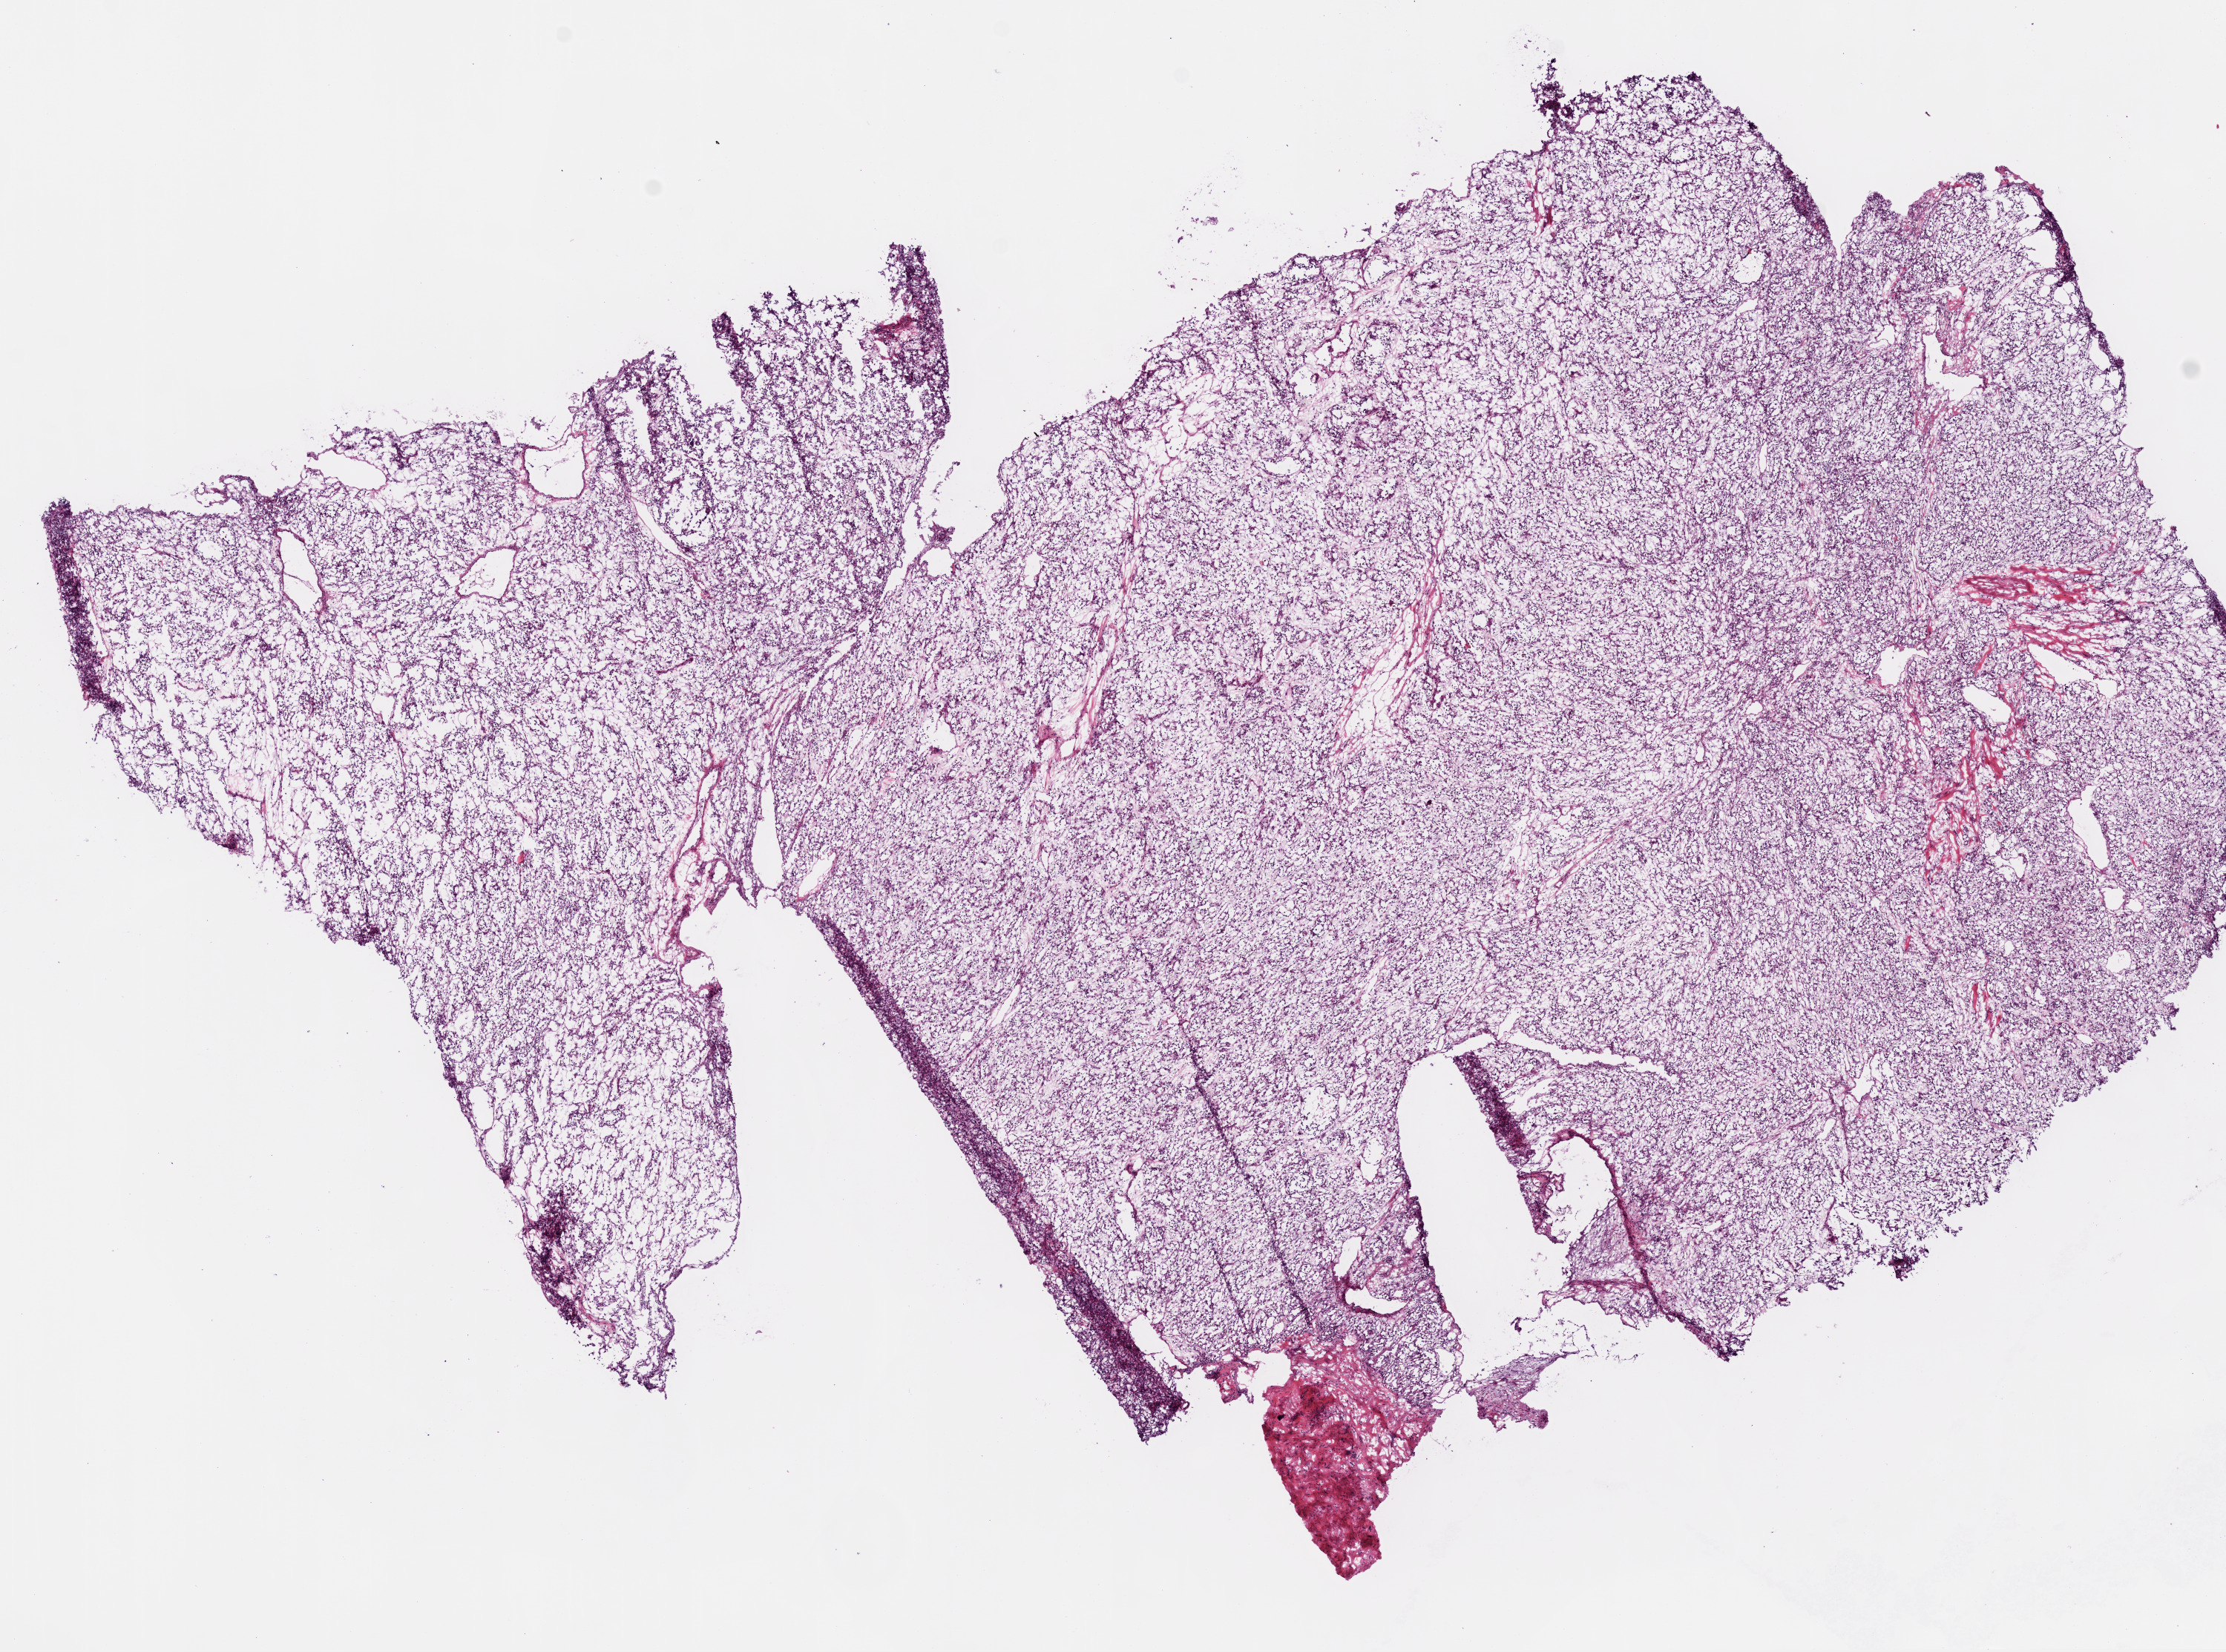
H&E whole-slide image — whole scanned area (about 12.0 x 8.9 mm) shown as a low-resolution overview; frozen section; primary tumour sample from the kidney. Patient: female, age at initial diagnosis 34 years. Histologic grade: G2 (moderately differentiated). Pathologist review of this section (percent, as recorded): tumour cells 95%, tumour nuclei 70%, normal cells 0%, stromal cells 5%, necrosis 0%.
Pathologic diagnosis: Clear cell adenocarcinoma, NOS. AJCC pathologic stage: I. Laterality: left.